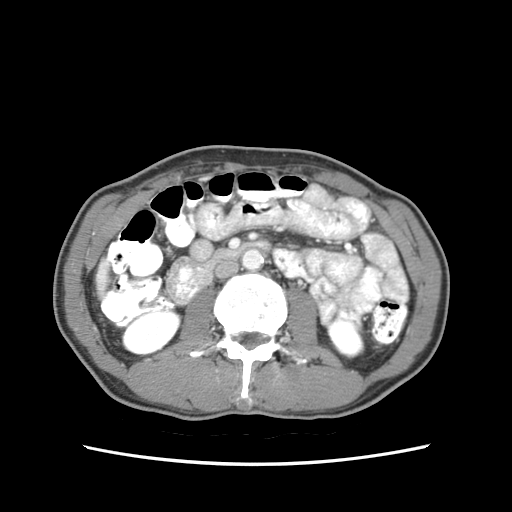
Contrast-enhanced abdominal CT (liver protocol), one axial slice; slice 8 of 79 in the series (ordered by position); reconstruction kernel STANDARD; 120 kVp; soft-tissue window (W 400 / L 40 HU); 2.5 mm slice thickness; 512 × 512 image matrix, field of view 320 × 320 mm. From the clinical record (not read from this slice): diagnosis: hepatocellular carcinoma (patient treated with transarterial chemoembolisation; whether this scan precedes or follows treatment is not stated here); TNM stage (as recorded): Stage-IIIB; Child-Pugh class: A.
Structures marked on this image (semi-automatically segmented with operator editing):
- liver parenchyma outside the tumour (the mass and vessels are separate outlines, so this box may not span the whole liver): box from (x=96, y=265) to (x=107, y=289) px